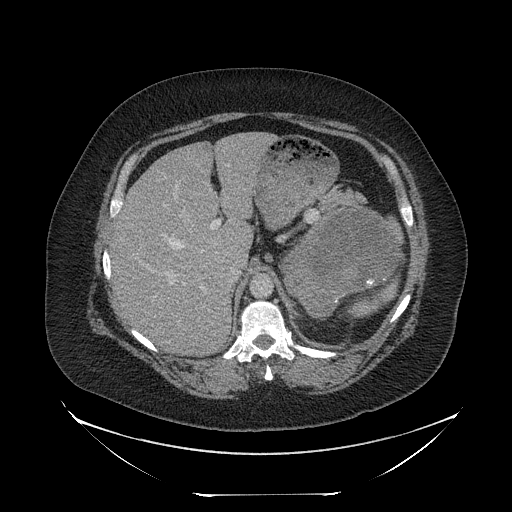
Contrast-enhanced abdominal CT, one axial slice; slice 160 of 205 in the series (ordered by position); reconstruction kernel STANDARD; intravenous contrast given; soft-tissue window (W 400 / L 40 HU); 2.5 mm slice thickness; 512 × 512 image matrix, field of view 500 × 500 mm. Patient: female, 53 years. From the clinical record (not read from this slice): diagnosis: adrenocortical carcinoma; tumour side: left adrenal; tumour size at pathology: 17 cm; Ki-67 index: 20 %; stage (as recorded): 3.
Structures marked on this image (semi-automatically segmented with operator editing):
- mass: bounding box <281,212,401,315> (left, top, right, bottom; pixels)